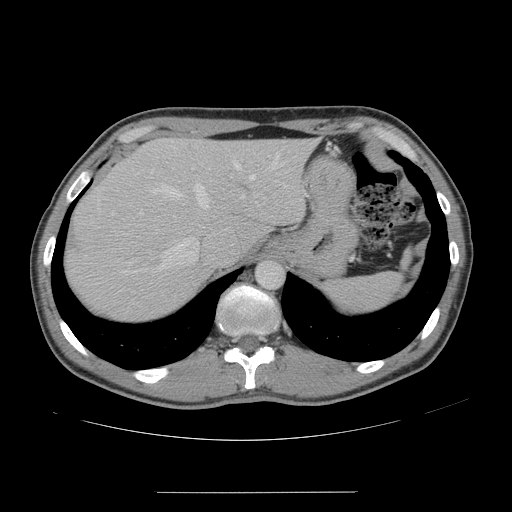
Contrast-enhanced abdominal CT, one axial slice; 120 kVp; intravenous contrast given; soft-tissue window (W 400 / L 40 HU); 2.5 mm slice thickness; 512 × 512 image matrix, field of view 401 × 401 mm. Male patient, age 53 years. From the clinical record (not read from this slice): diagnosis: colorectal cancer liver metastases, imaged before liver resection; multiple liver metastases: yes; largest metastasis: 2.4 cm; disease in both lobes: no.
Structures marked on this image (outlined manually by an expert reader):
- hepatic veins: box from (x=150, y=153) to (x=279, y=270) px
- liver: (x=66, y=139)–(x=314, y=320)
- planned liver remnant (the part of the liver to remain after resection): (x=148, y=139)–(x=314, y=246)
- portal vein (with intrahepatic branches): (x=139, y=210)–(x=143, y=215)